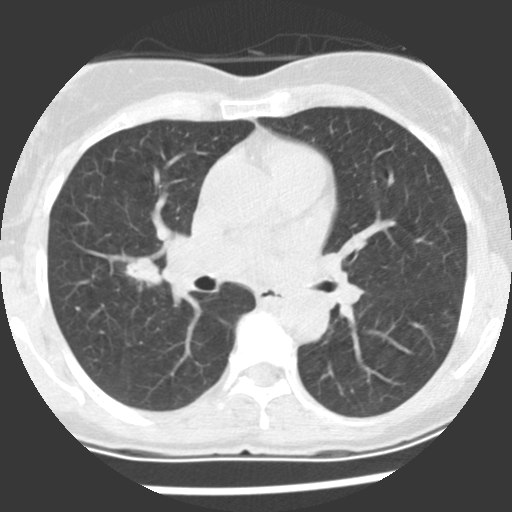
Low-dose screening chest CT, one axial slice. Position 122 of 225 along the scan axis. Reconstruction kernel STANDARD. 120 kVp. Lung window (W 1500 / L -600 HU). 2.5 mm slice thickness. 512 × 512 image matrix.
Annotated regions visible in this slice (expert manual segmentation):
- lesion 1 (tumor, upper lobe of right lung): bounding box [x1, y1, x2, y2] px = [125, 257, 163, 290]